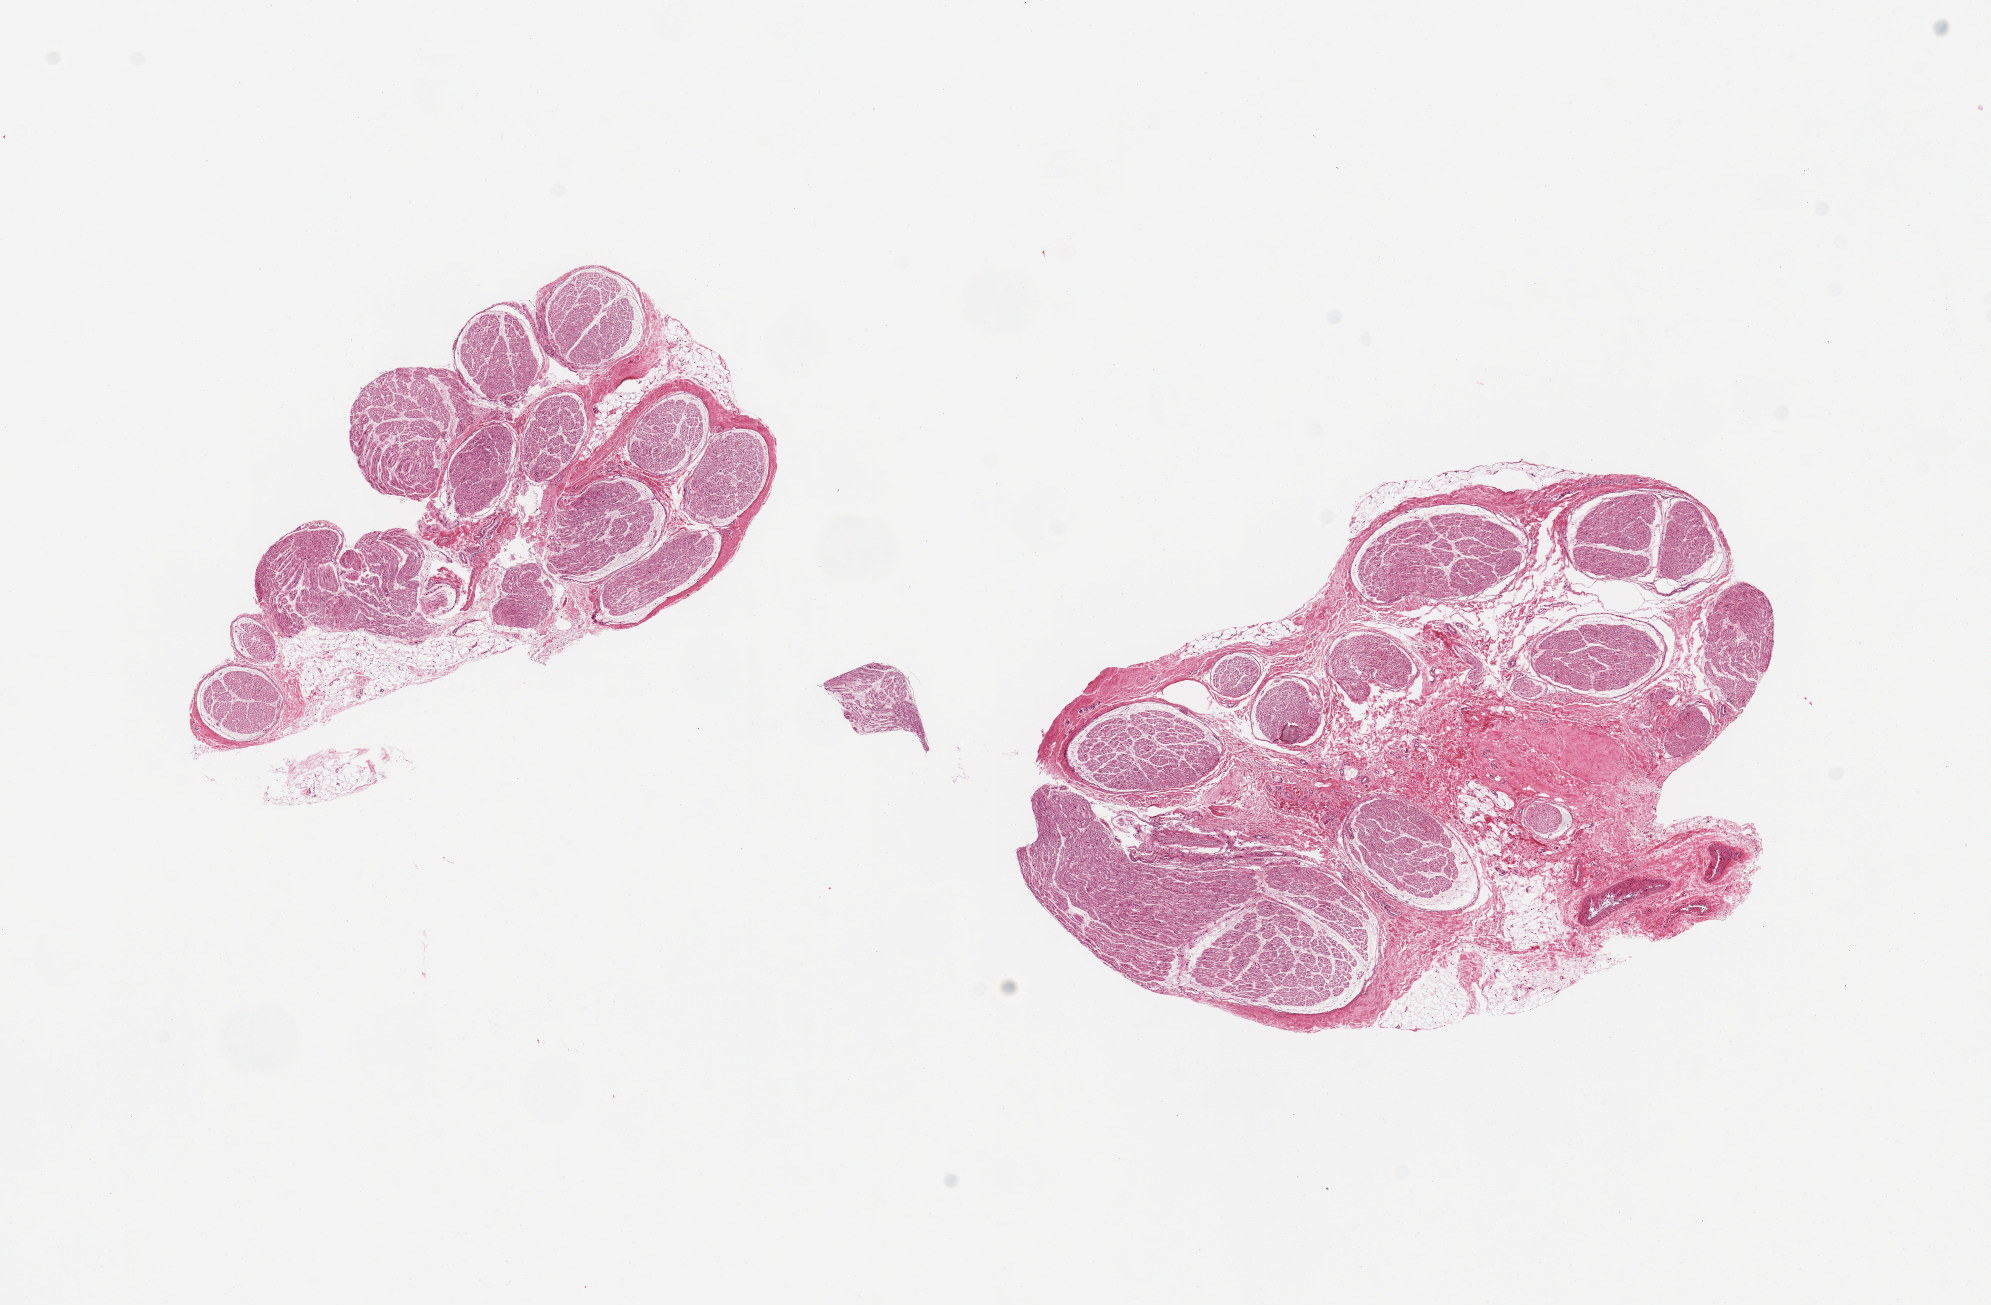
Whole-slide image, haematoxylin and eosin stain, brightfield — a low-resolution overview of the entire scanned area, about 15.8 x 10.3 mm; PAXgene-fixed, paraffin-embedded tissue; sampled site (target tissue): tibial nerve; donor tissue sample. Female donor.
Reviewer comment on this tissue sample: 2 pieces; includes 5-10% attached fat.